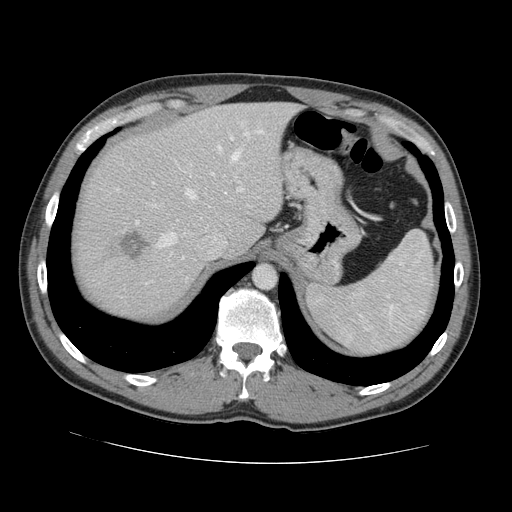
Contrast-enhanced abdominal CT, one axial slice; position 106 of 131 along the scan axis; 120 kVp; intravenous contrast given; soft-tissue window (W 400 / L 40 HU); 512 × 512 image matrix, field of view 380 × 380 mm. Male patient, age 40 years. Case-level facts recorded for this patient, not image findings: diagnosis: colorectal cancer liver metastases, imaged before liver resection; multiple liver metastases: yes; largest metastasis: 2.9 cm; disease in both lobes: yes.
Structures marked on this image (manually delineated by an expert):
- hepatic veins: bounding box [x1, y1, x2, y2] px = [158, 146, 240, 247]
- liver: [74, 104, 294, 318]
- planned liver remnant (the part of the liver to remain after resection): [101, 103, 296, 255]
- portal vein (with intrahepatic branches): [211, 132, 261, 192]
- liver metastasis: [119, 231, 150, 260]